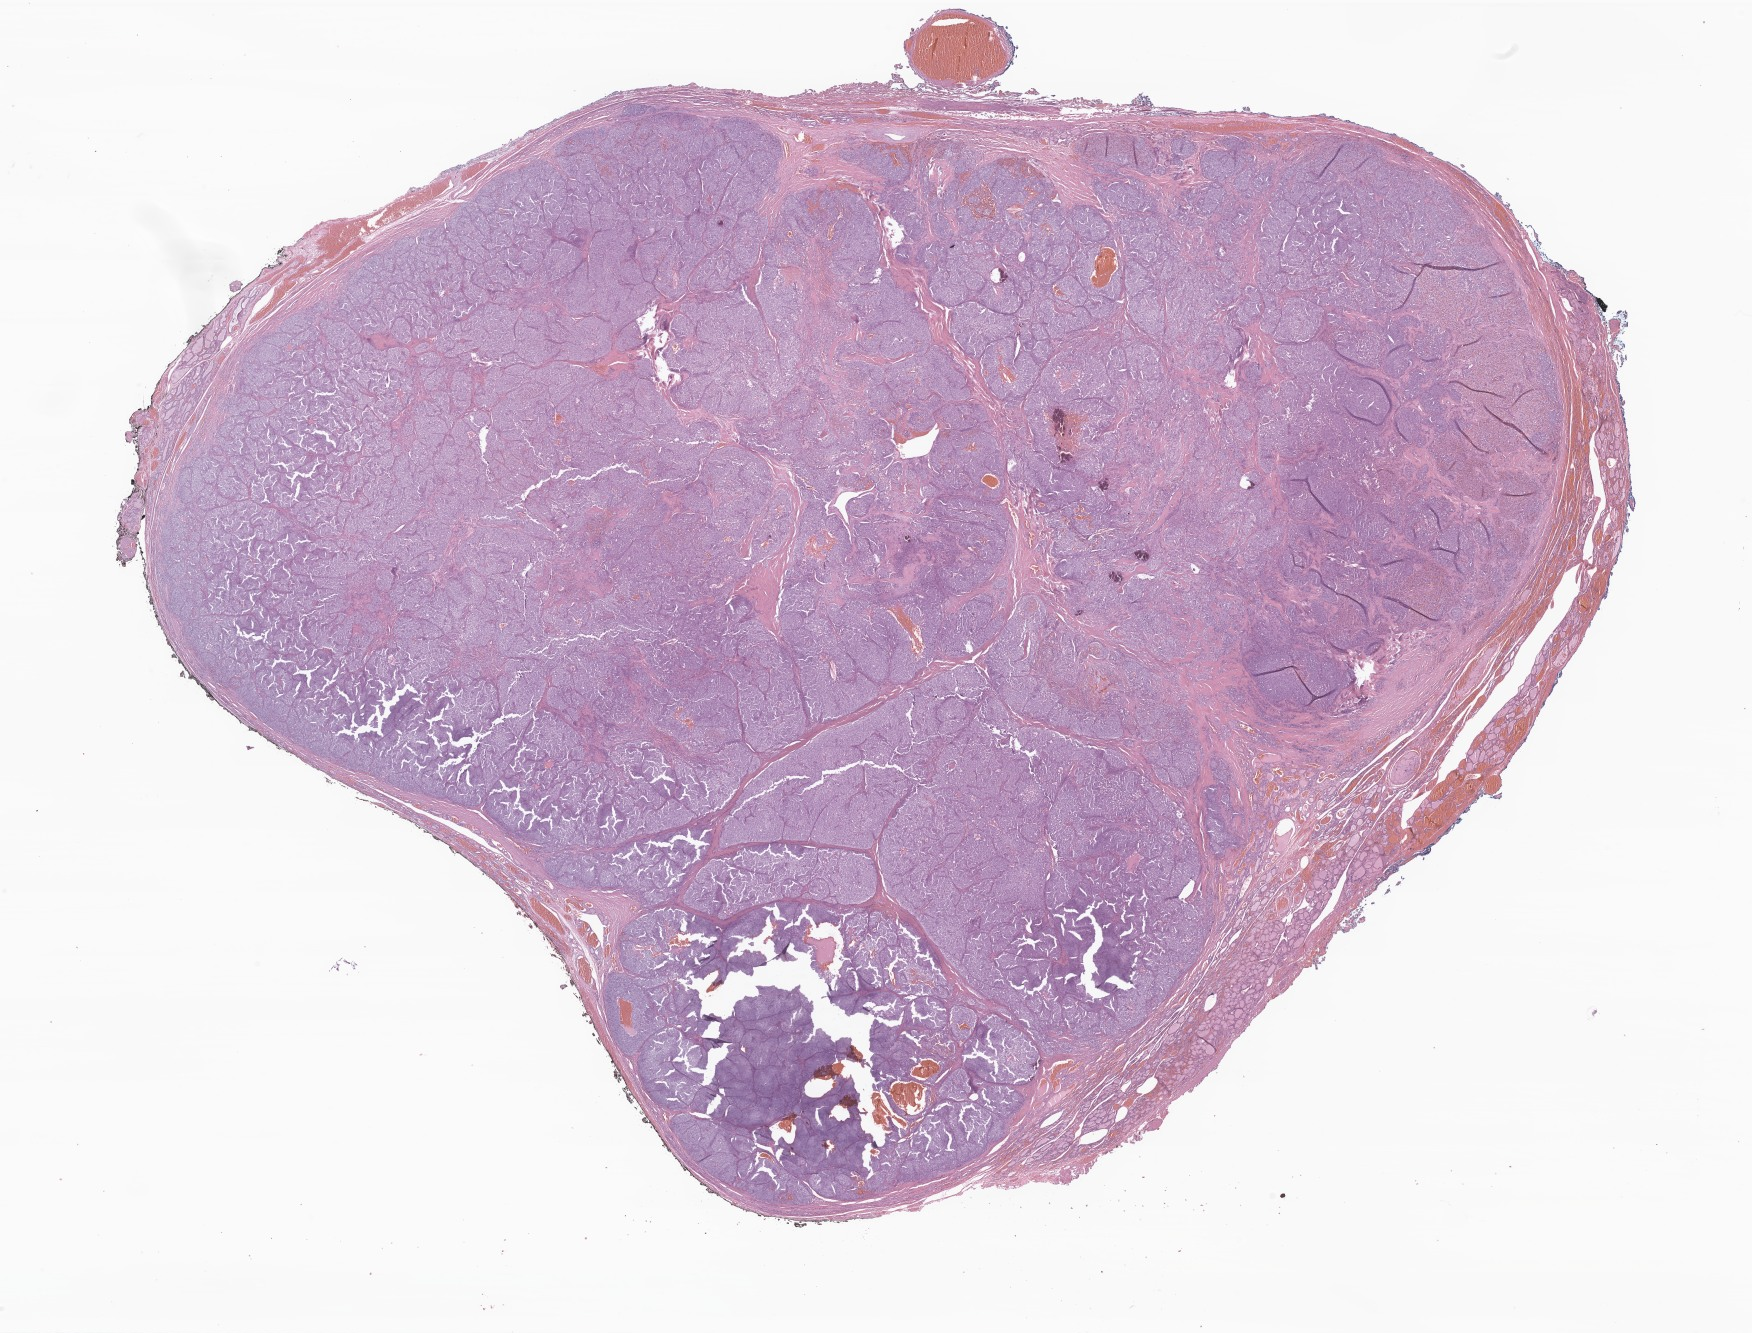
Whole-slide image, haematoxylin and eosin stain of tumor tissue from the thyroid, low-resolution overview of the scanned area, about 29.6 x 22.5 mm, FFPE section. Patient male; age 120 months (10 years).
• recorded diagnosis: Medullary carcinoma, NOS